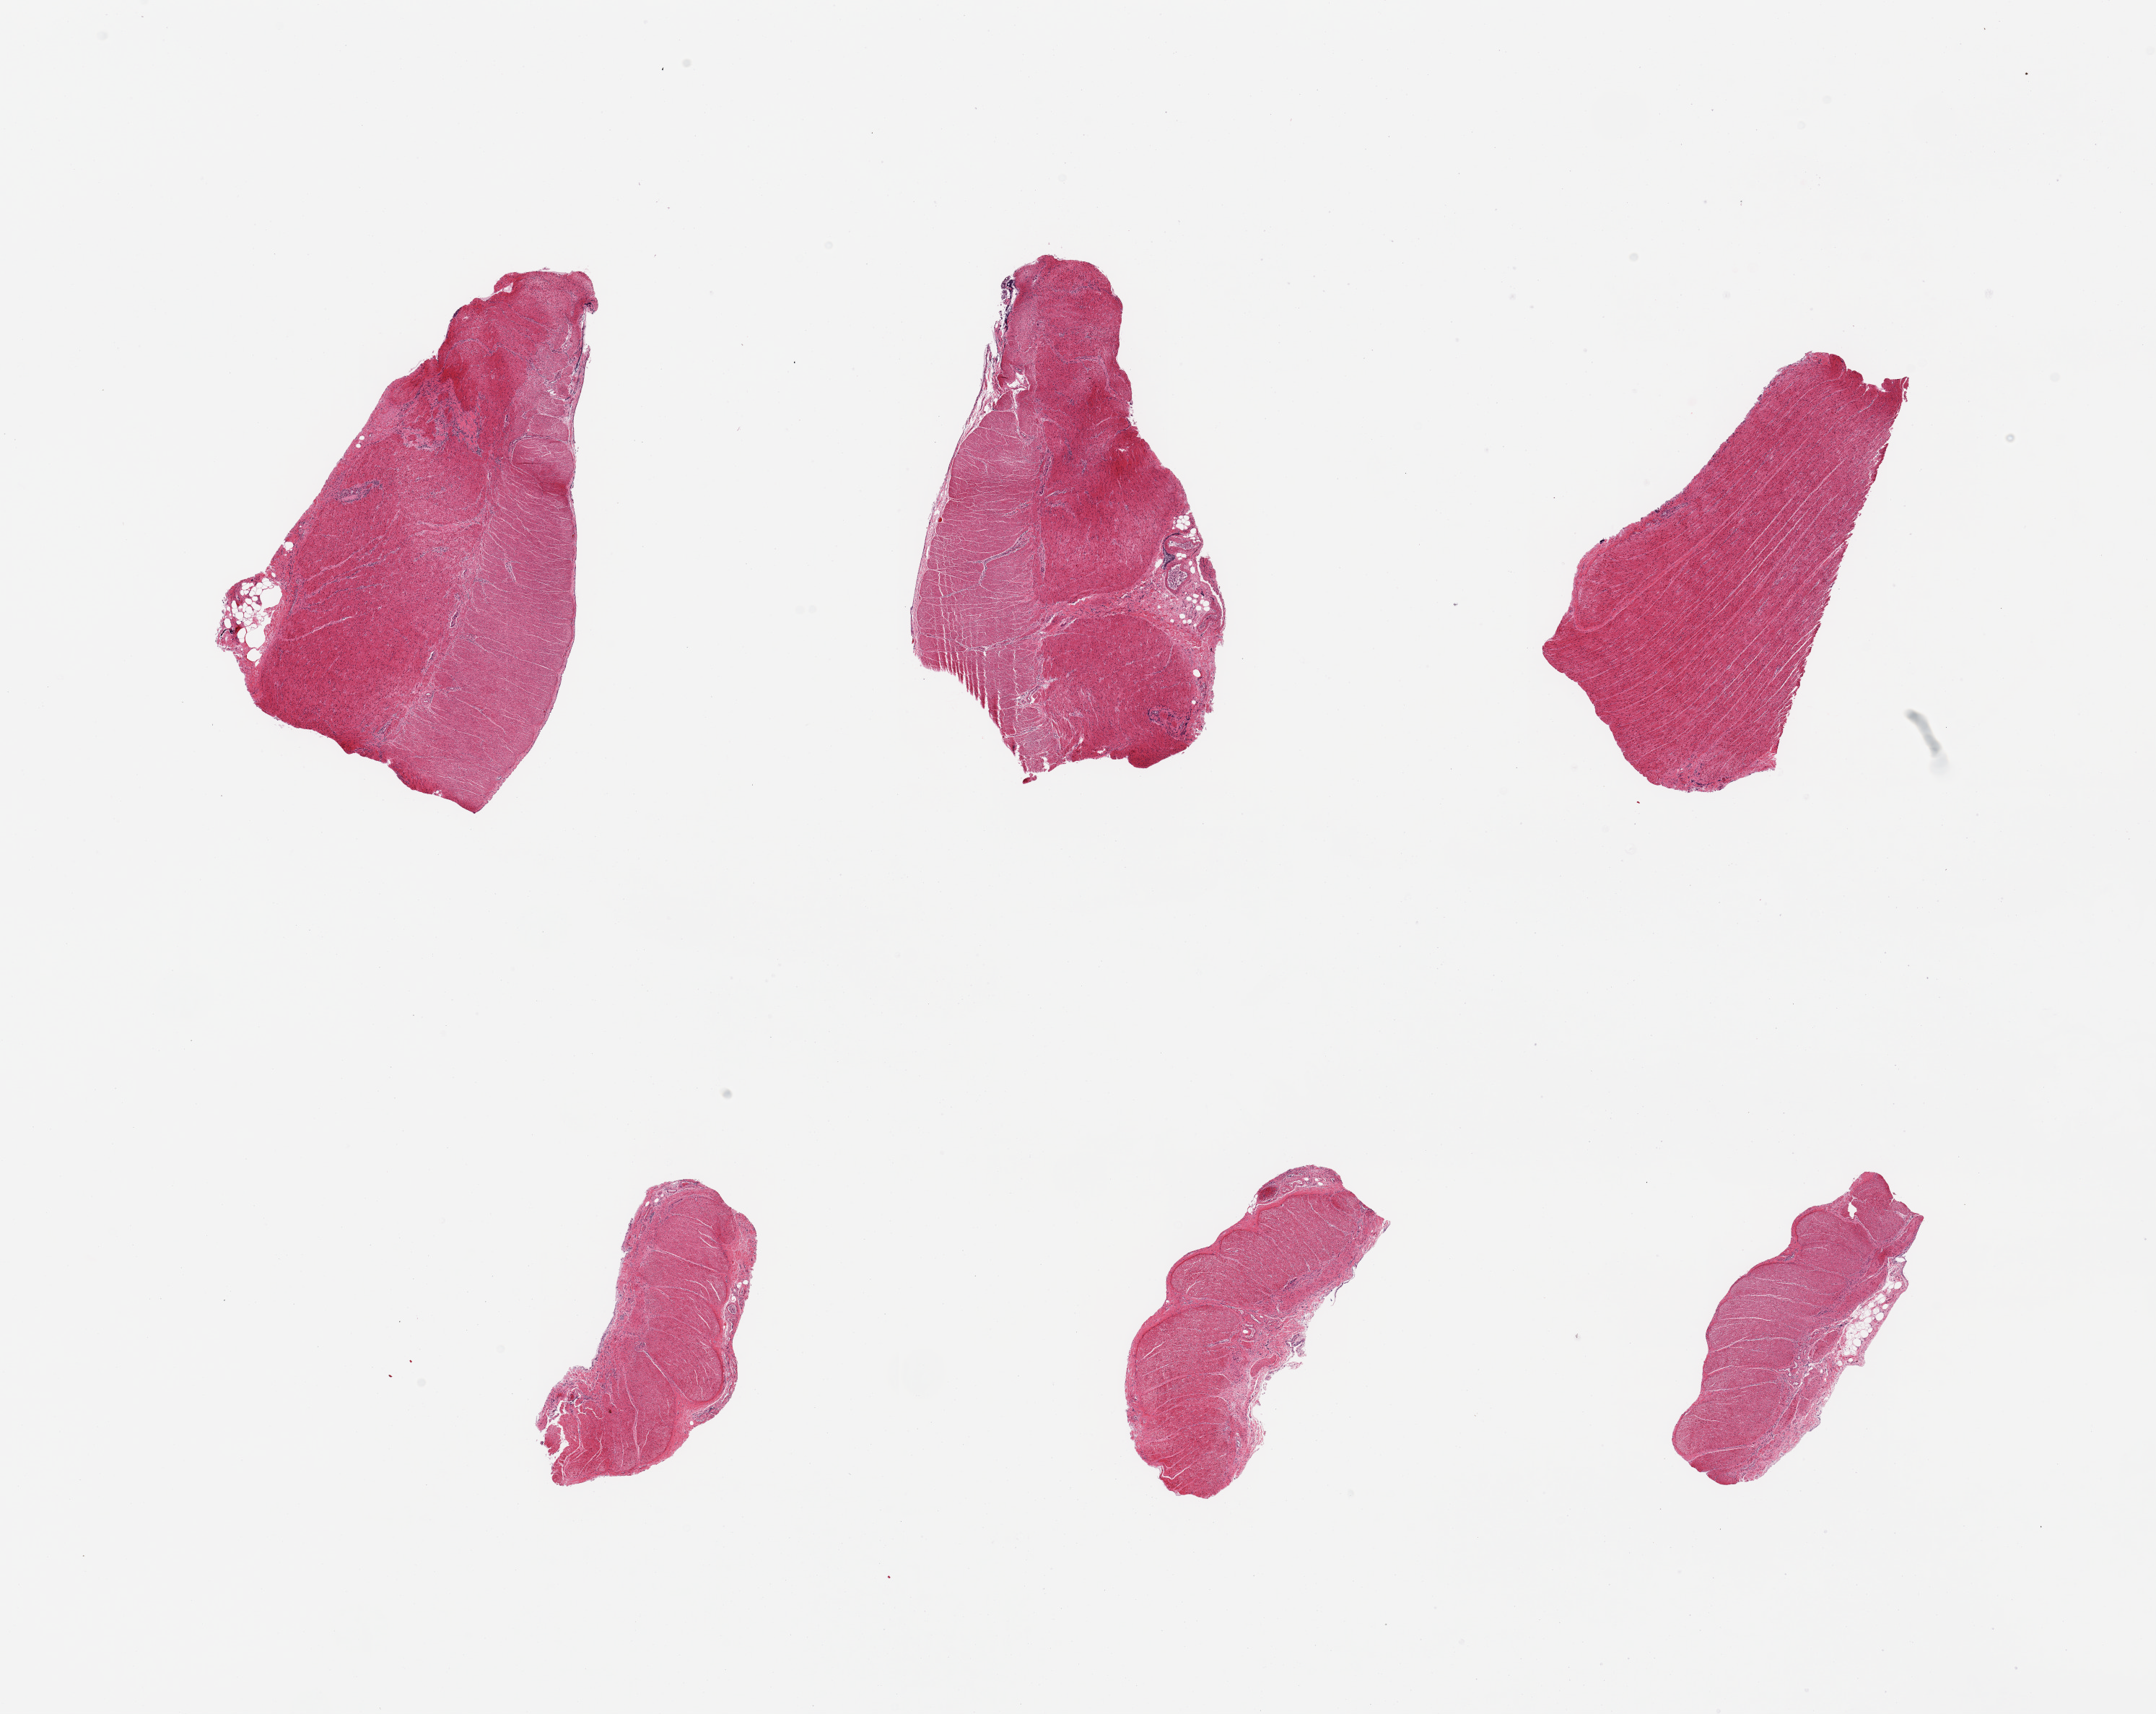
Whole-slide image, hematoxylin and eosin (H&E) stain, brightfield — a low-resolution overview of the entire scanned area, about 23.6 x 18.8 mm (acquisition: 20x scan), PAXgene-fixed, paraffin-embedded tissue, target tissue: sigmoid colon, tissue donor sample. Donor: male.
Review note (as recorded): 6 pieces, target muscularis.